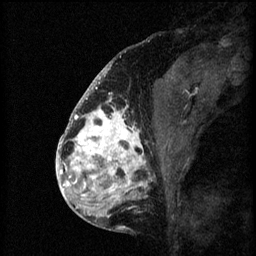
Breast MRI (dynamic contrast-enhanced), one sagittal slice; position 28 of 60 along the scan axis; 3 images stored at this slice position (order not interpretable as contrast timing); 1.5 T; TE 4.2 ms, TR 8.2 ms; 2 mm slice thickness; 256 × 256 image matrix. Patient: female, 41 years.
Structures marked on this image (semi-automatic segmentation, software-assisted and operator-edited):
- analysis volume of interest (the breast-tissue region the enhancement analysis was run in; not a lesion): bounding box (x1, y1, x2, y2) in pixels: (72, 108, 176, 205)
- tumour enhancement mask (voxels above the 70 % enhancement threshold inside the analysis volume of interest): (72, 108, 149, 203)